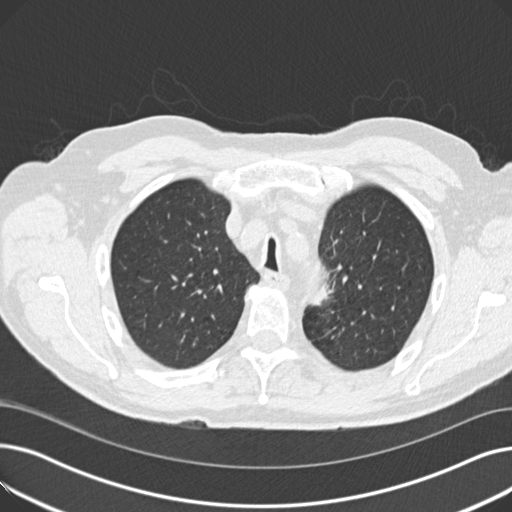
Low-dose screening chest CT, one axial slice. Slice 143 of 191 in the series (ordered by position). Reconstruction kernel B30f. 120 kVp. Lung window (W 1500 / L -600 HU). 2 mm slice thickness. 512 × 512 image matrix, field of view 370 × 370 mm.
Outlined on this slice (outlined manually by an expert reader):
- lesion 1 (tumor, upper lobe of left lung): box from (x=310, y=281) to (x=334, y=305) px